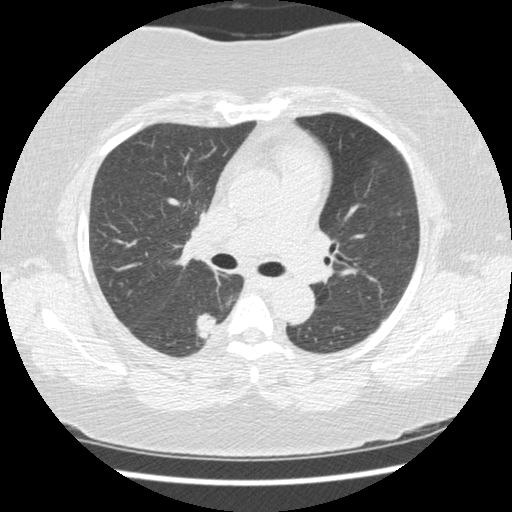
Low-dose screening chest CT, axial slice; second annual screen; lung window (W 1500 / L -600 HU); 1.25 mm slice thickness; standard (soft-tissue) reconstruction kernel (STANDARD); 120 kVp; 512 × 512 image matrix, field of view 331 × 331 mm. Female participant, aged 58 years at enrolment.
Expert-annotated lung lesion, bounding box [x1, y1, x2, y2] px = [189, 308, 229, 353]. Screening reader's record for this exam (one nodule recorded; not confirmed to be the boxed lesion): non-calcified nodule or mass ≥4 mm, right lower lobe, 15 × 15 mm, spiculated (stellate) margins, soft tissue attenuation, pre-existing on the prior screen: yes; interval growth: yes. Participant outcome: lung cancer diagnosed 21 days after this screen — adenocarcinoma, NOS, right lower lobe, stage IB (AJCC 6th edition), 15 mm at pathology.